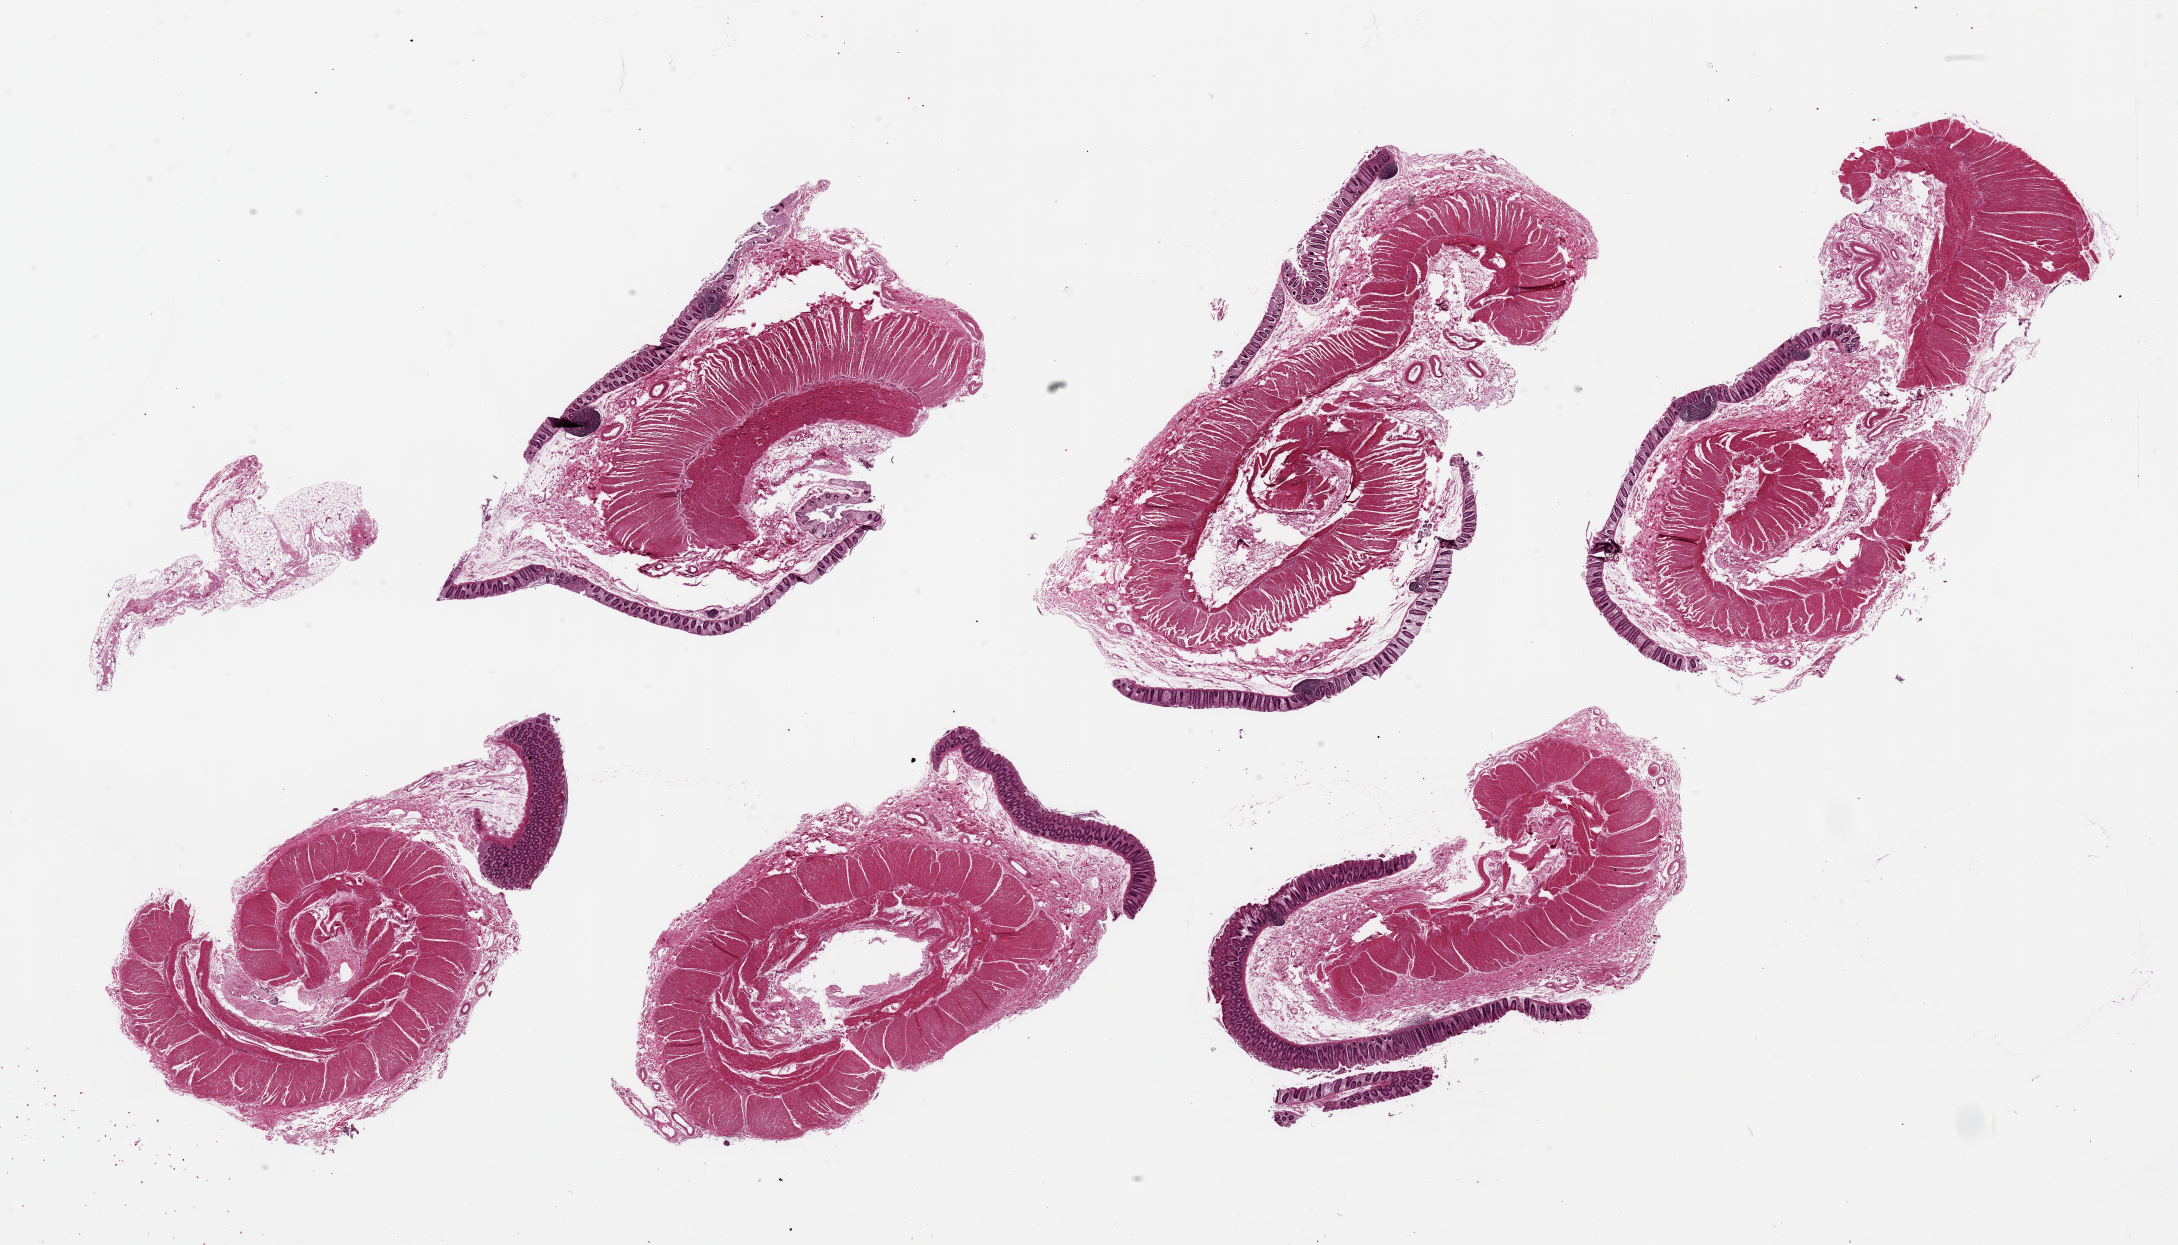
Whole-slide image, H&E stain, brightfield — shown as a low-resolution overview of the whole scanned area (about 34.5 x 19.7 mm, acquisition: 20x scan); PAXgene-fixed, paraffin-embedded tissue; section of transverse colon (target tissue); donor tissue sample. Donor sex: female.
Review note (as recorded): 6 pieces, ~7x4mm fragmented/detached msucosa but fairly well preserved, up to 10% thickness.